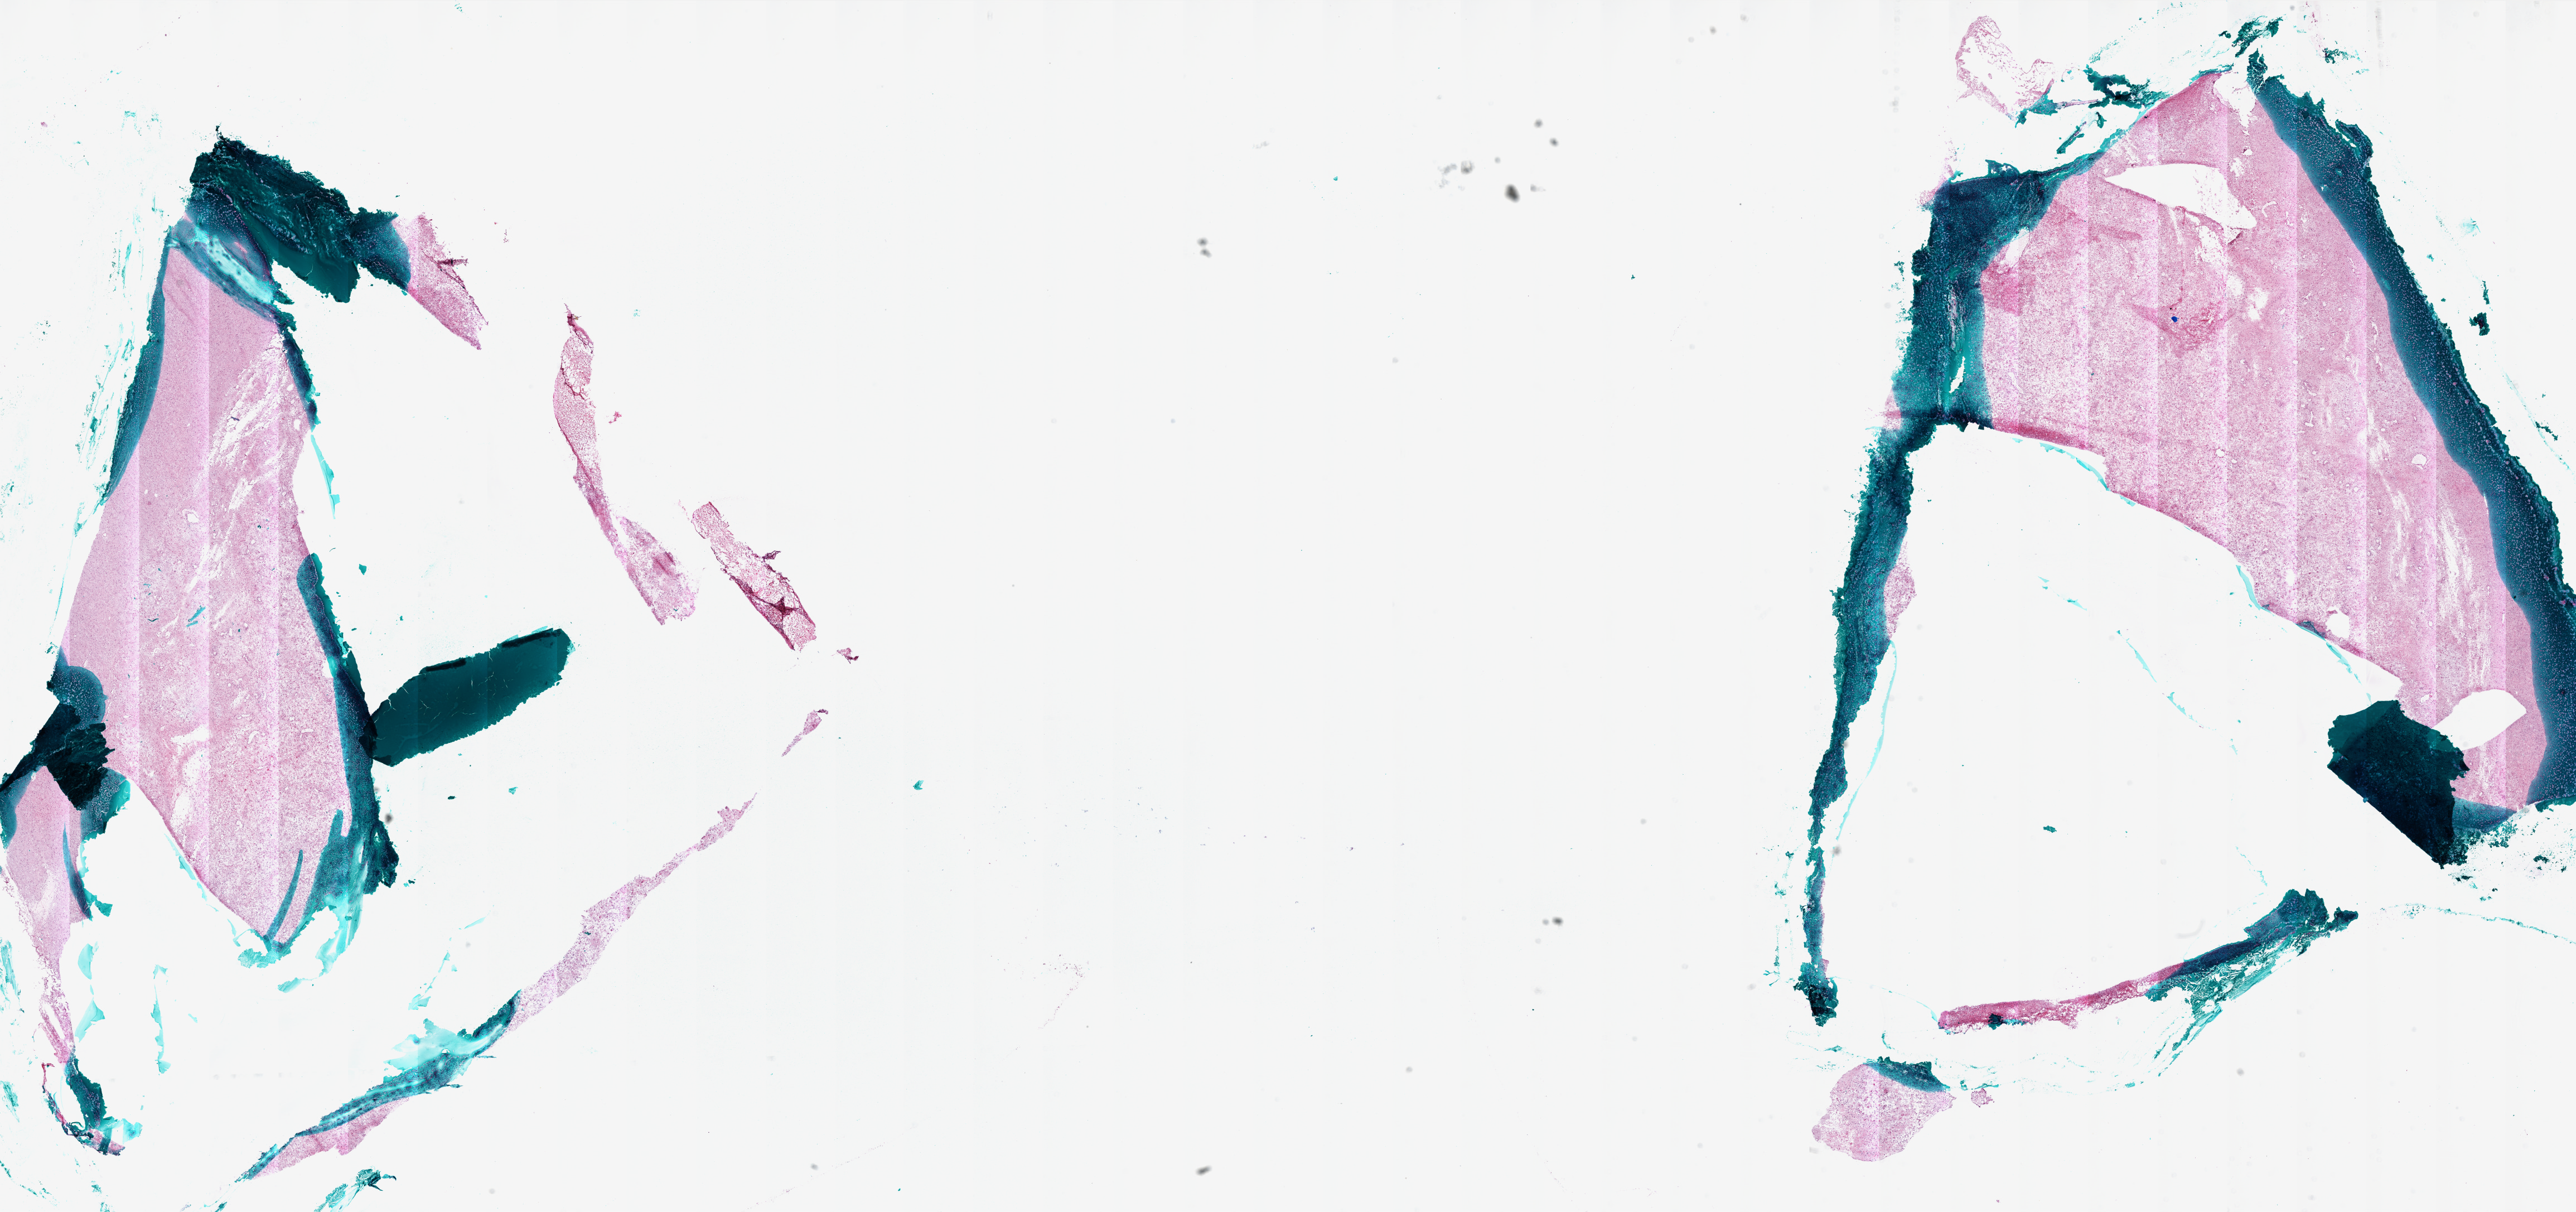
Digitized H&E-stained tissue section (whole slide), shown as a low-resolution overview of the whole scanned area (about 37.0 x 17.4 mm, from a 20x scan), frozen section, primary tumour sample from the brain. Male, age 78 years at initial diagnosis. Composition of this section per pathologist review: tumour cells 75%, tumour nuclei 95%, normal cells 0%, stromal cells 20%, necrosis 5%.
Pathologic diagnosis: Glioblastoma.